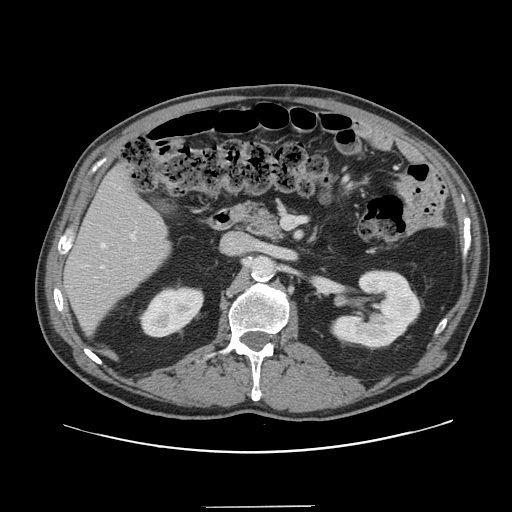
Contrast-enhanced abdominal CT, one axial slice. Slice 69 of 139 in the series (ordered by position). 120 kVp. Intravenous contrast given. Soft-tissue window (W 400 / L 40 HU). 2.5 mm slice thickness. 512 × 512 image matrix, field of view 397 × 397 mm. Male patient, age 64 years. Case-level facts recorded for this patient, not image findings: diagnosis: colorectal cancer liver metastases, imaged before liver resection; multiple liver metastases: yes; largest metastasis: 3.5 cm; disease in both lobes: yes.
Outlined on this slice (manually delineated by an expert):
- hepatic veins: bounding box <101,243,105,269> (left, top, right, bottom; pixels)
- liver: <66,169,167,330>
- planned liver remnant (the part of the liver to remain after resection): <65,170,168,331>
- portal vein (with intrahepatic branches): <131,234,135,240>